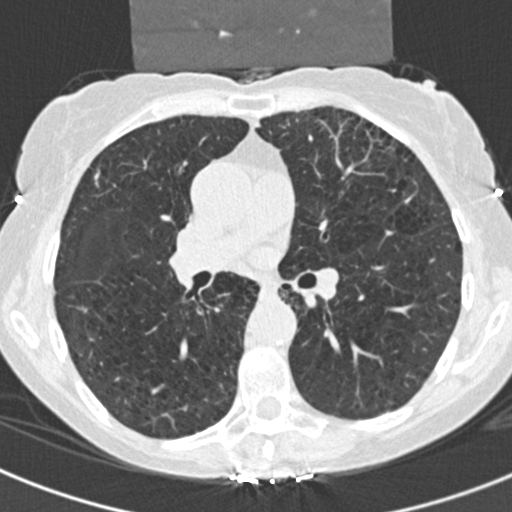
Low-dose screening chest CT, one axial slice; position 108 of 181 along the scan axis; reconstruction kernel B30f; 120 kVp; lung window (W 1500 / L -600 HU); 512 × 512 image matrix, field of view 298 × 298 mm.
Structures marked on this image (expert manual segmentation):
- lesion 1 (tumor, upper lobe of right lung): bounding box <94,169,100,180> (left, top, right, bottom; pixels)